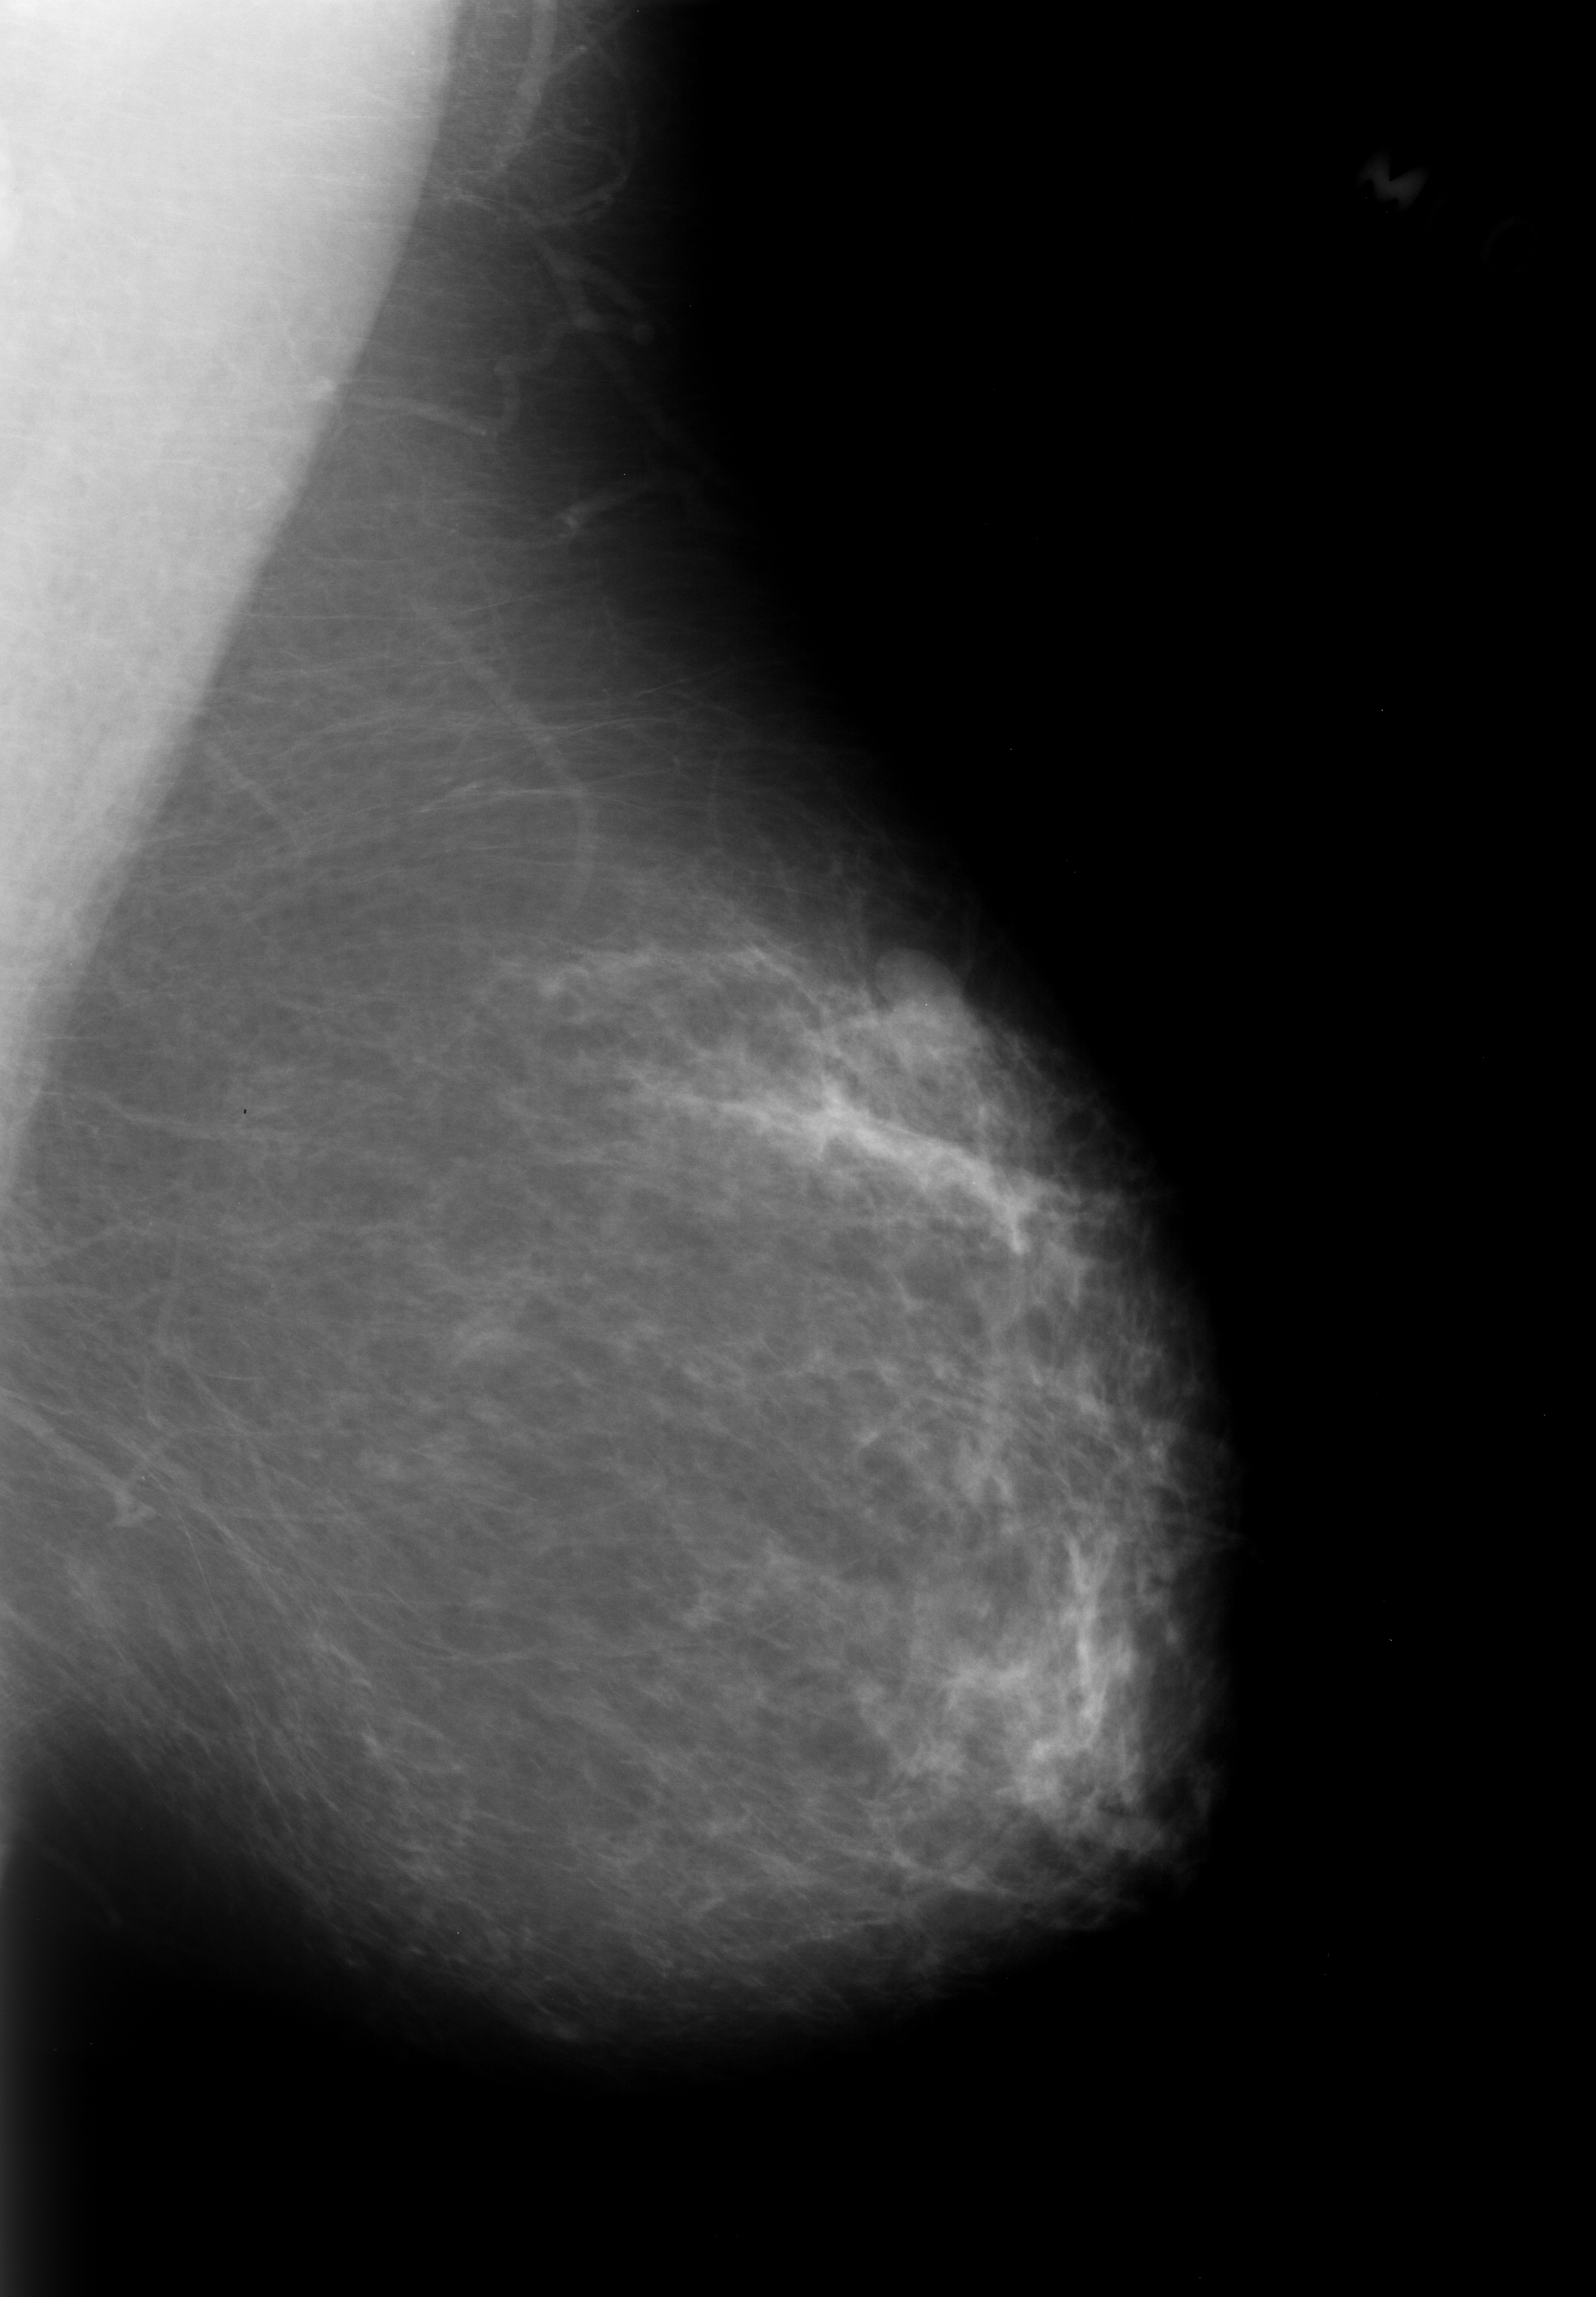
Mammogram (digitized film), left breast, MLO view, breast composition: almost entirely fatty (BI-RADS density category 1 of 4).
Radiologist-marked abnormalities on this image: mass, shape lobulated, margins obscured; BI-RADS assessment category 3; subtlety rating 5 on a 1 (subtle) to 5 (obvious) scale; pathology result (as recorded, not read from the image): benign.